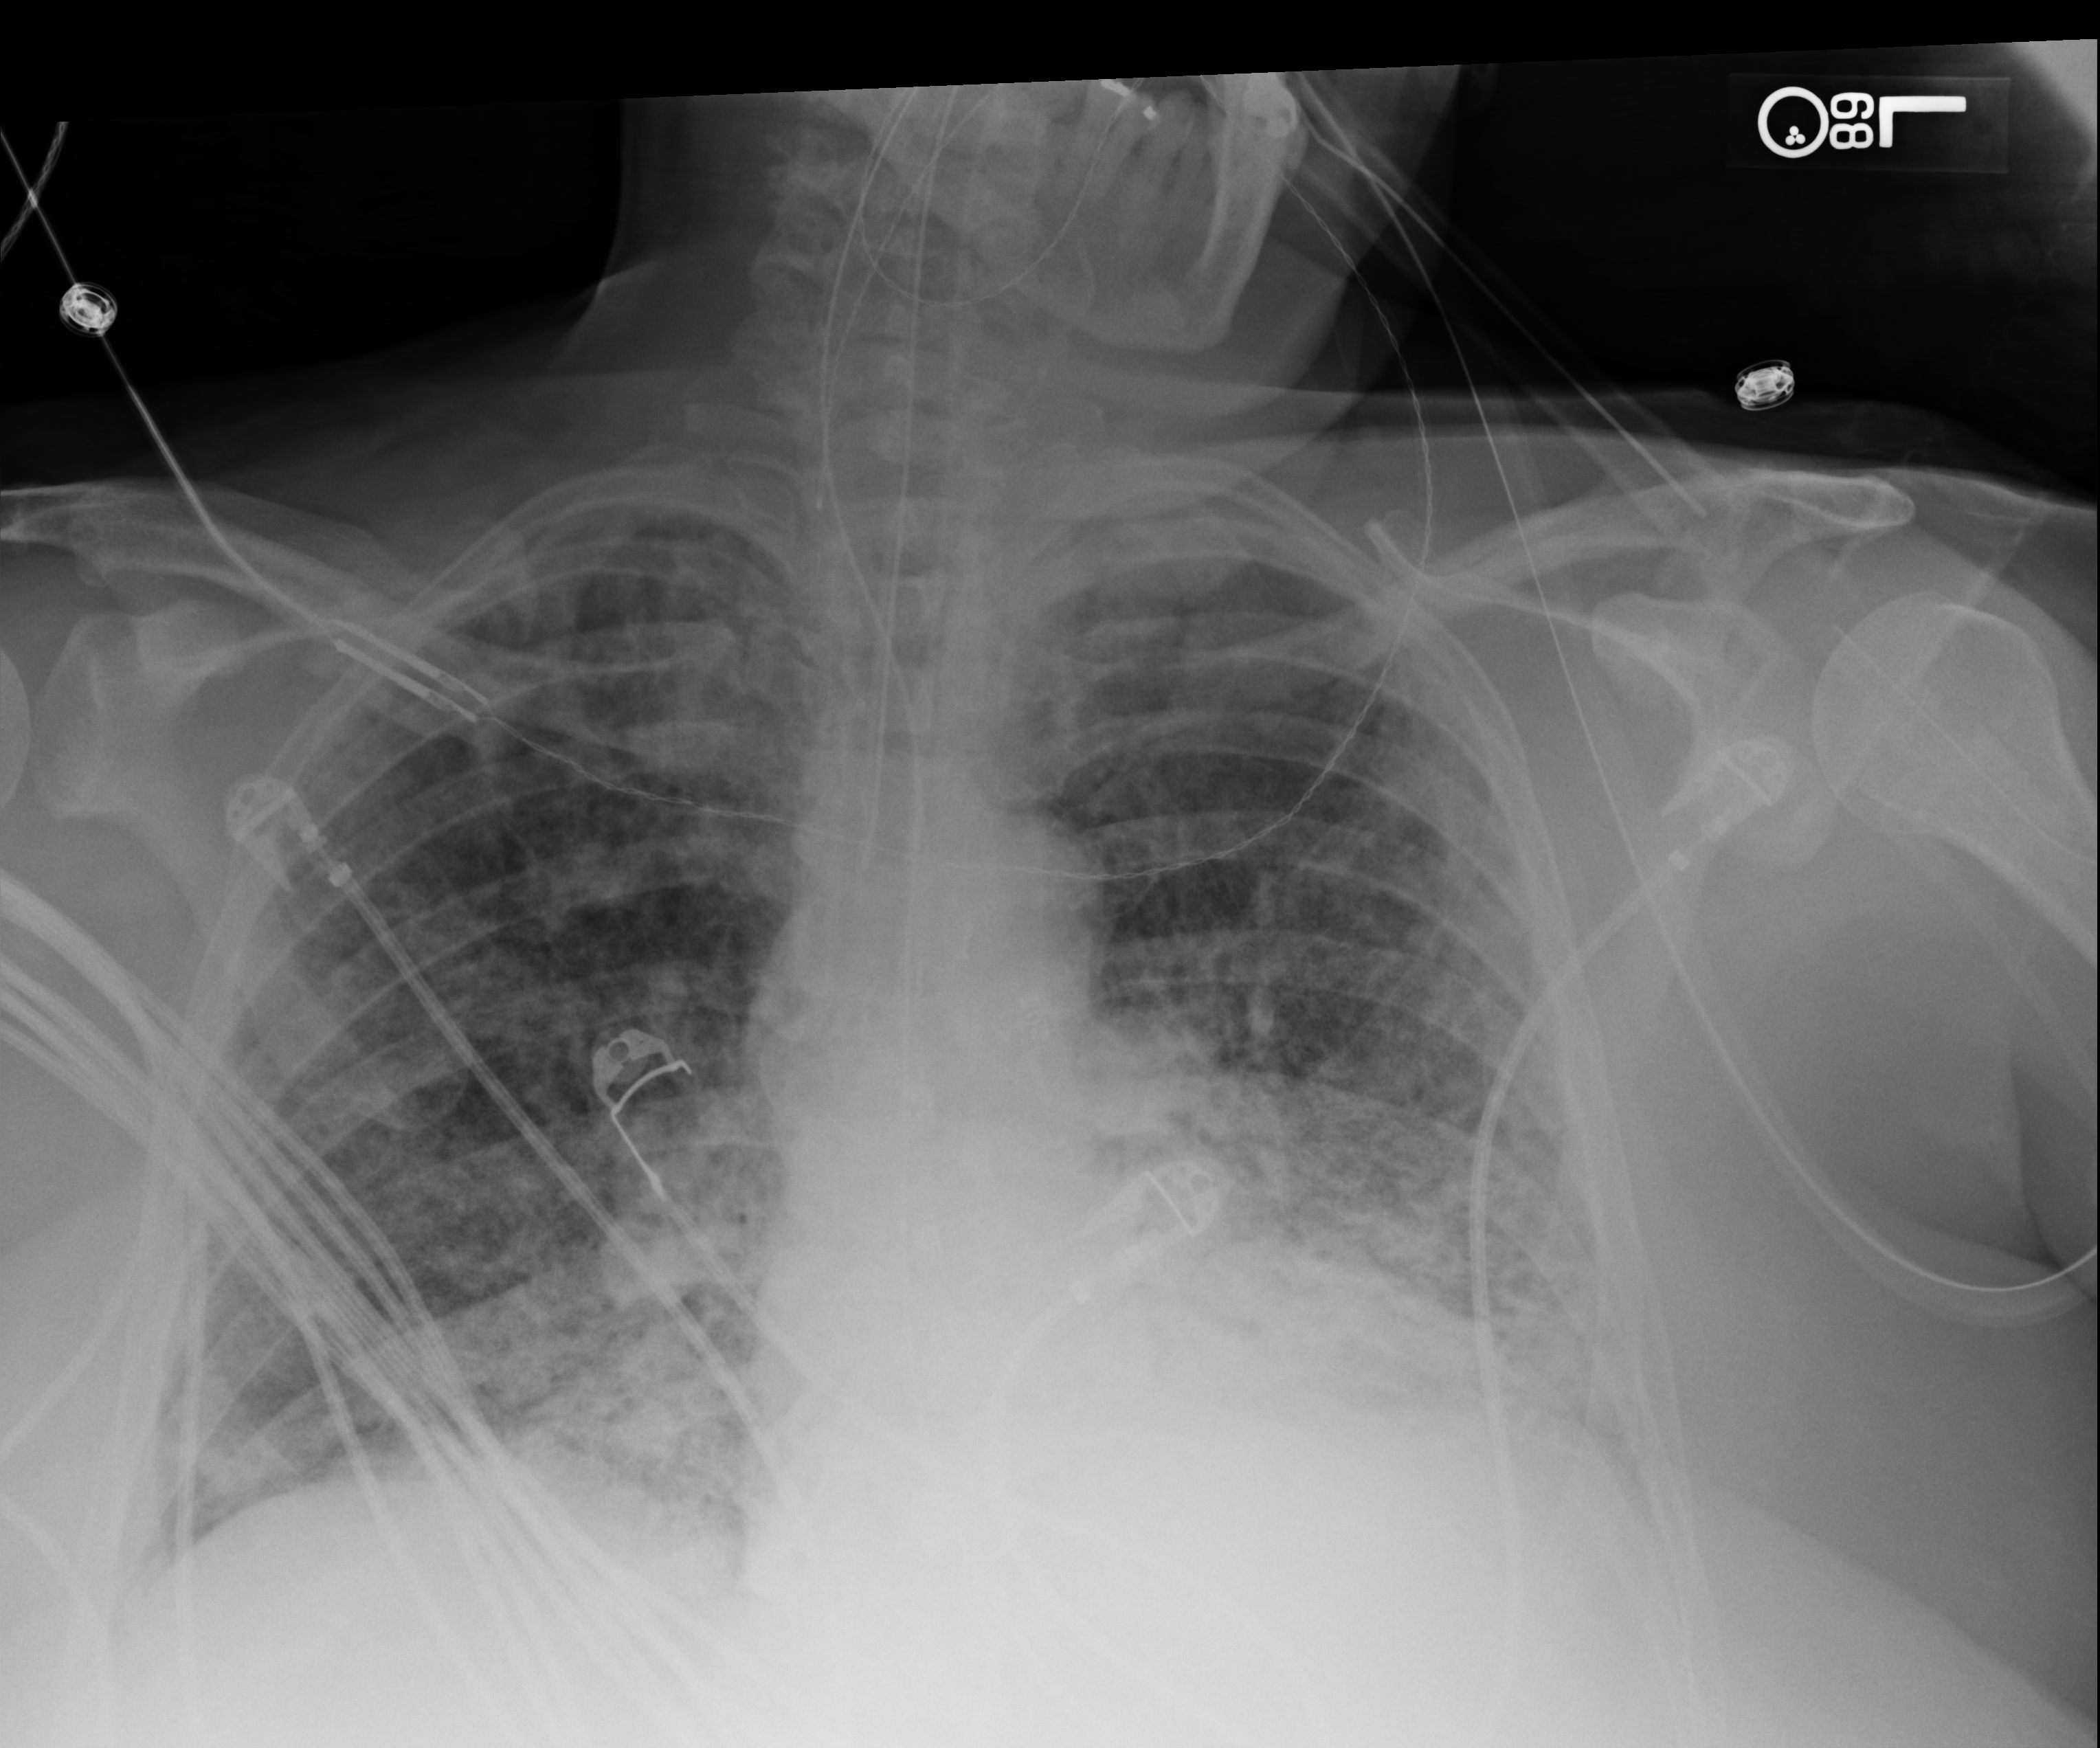
Portable chest radiograph, anteroposterior (AP) projection. Patient hospitalised with COVID-19, aged 18–59 years.
Hospital-stay facts (about this admission, not read from this image; timing relative to this image not recorded):
- mechanically ventilated during this hospital stay: yes
- admitted to intensive care during this hospital stay: yes
- length of hospital stay: 28 days